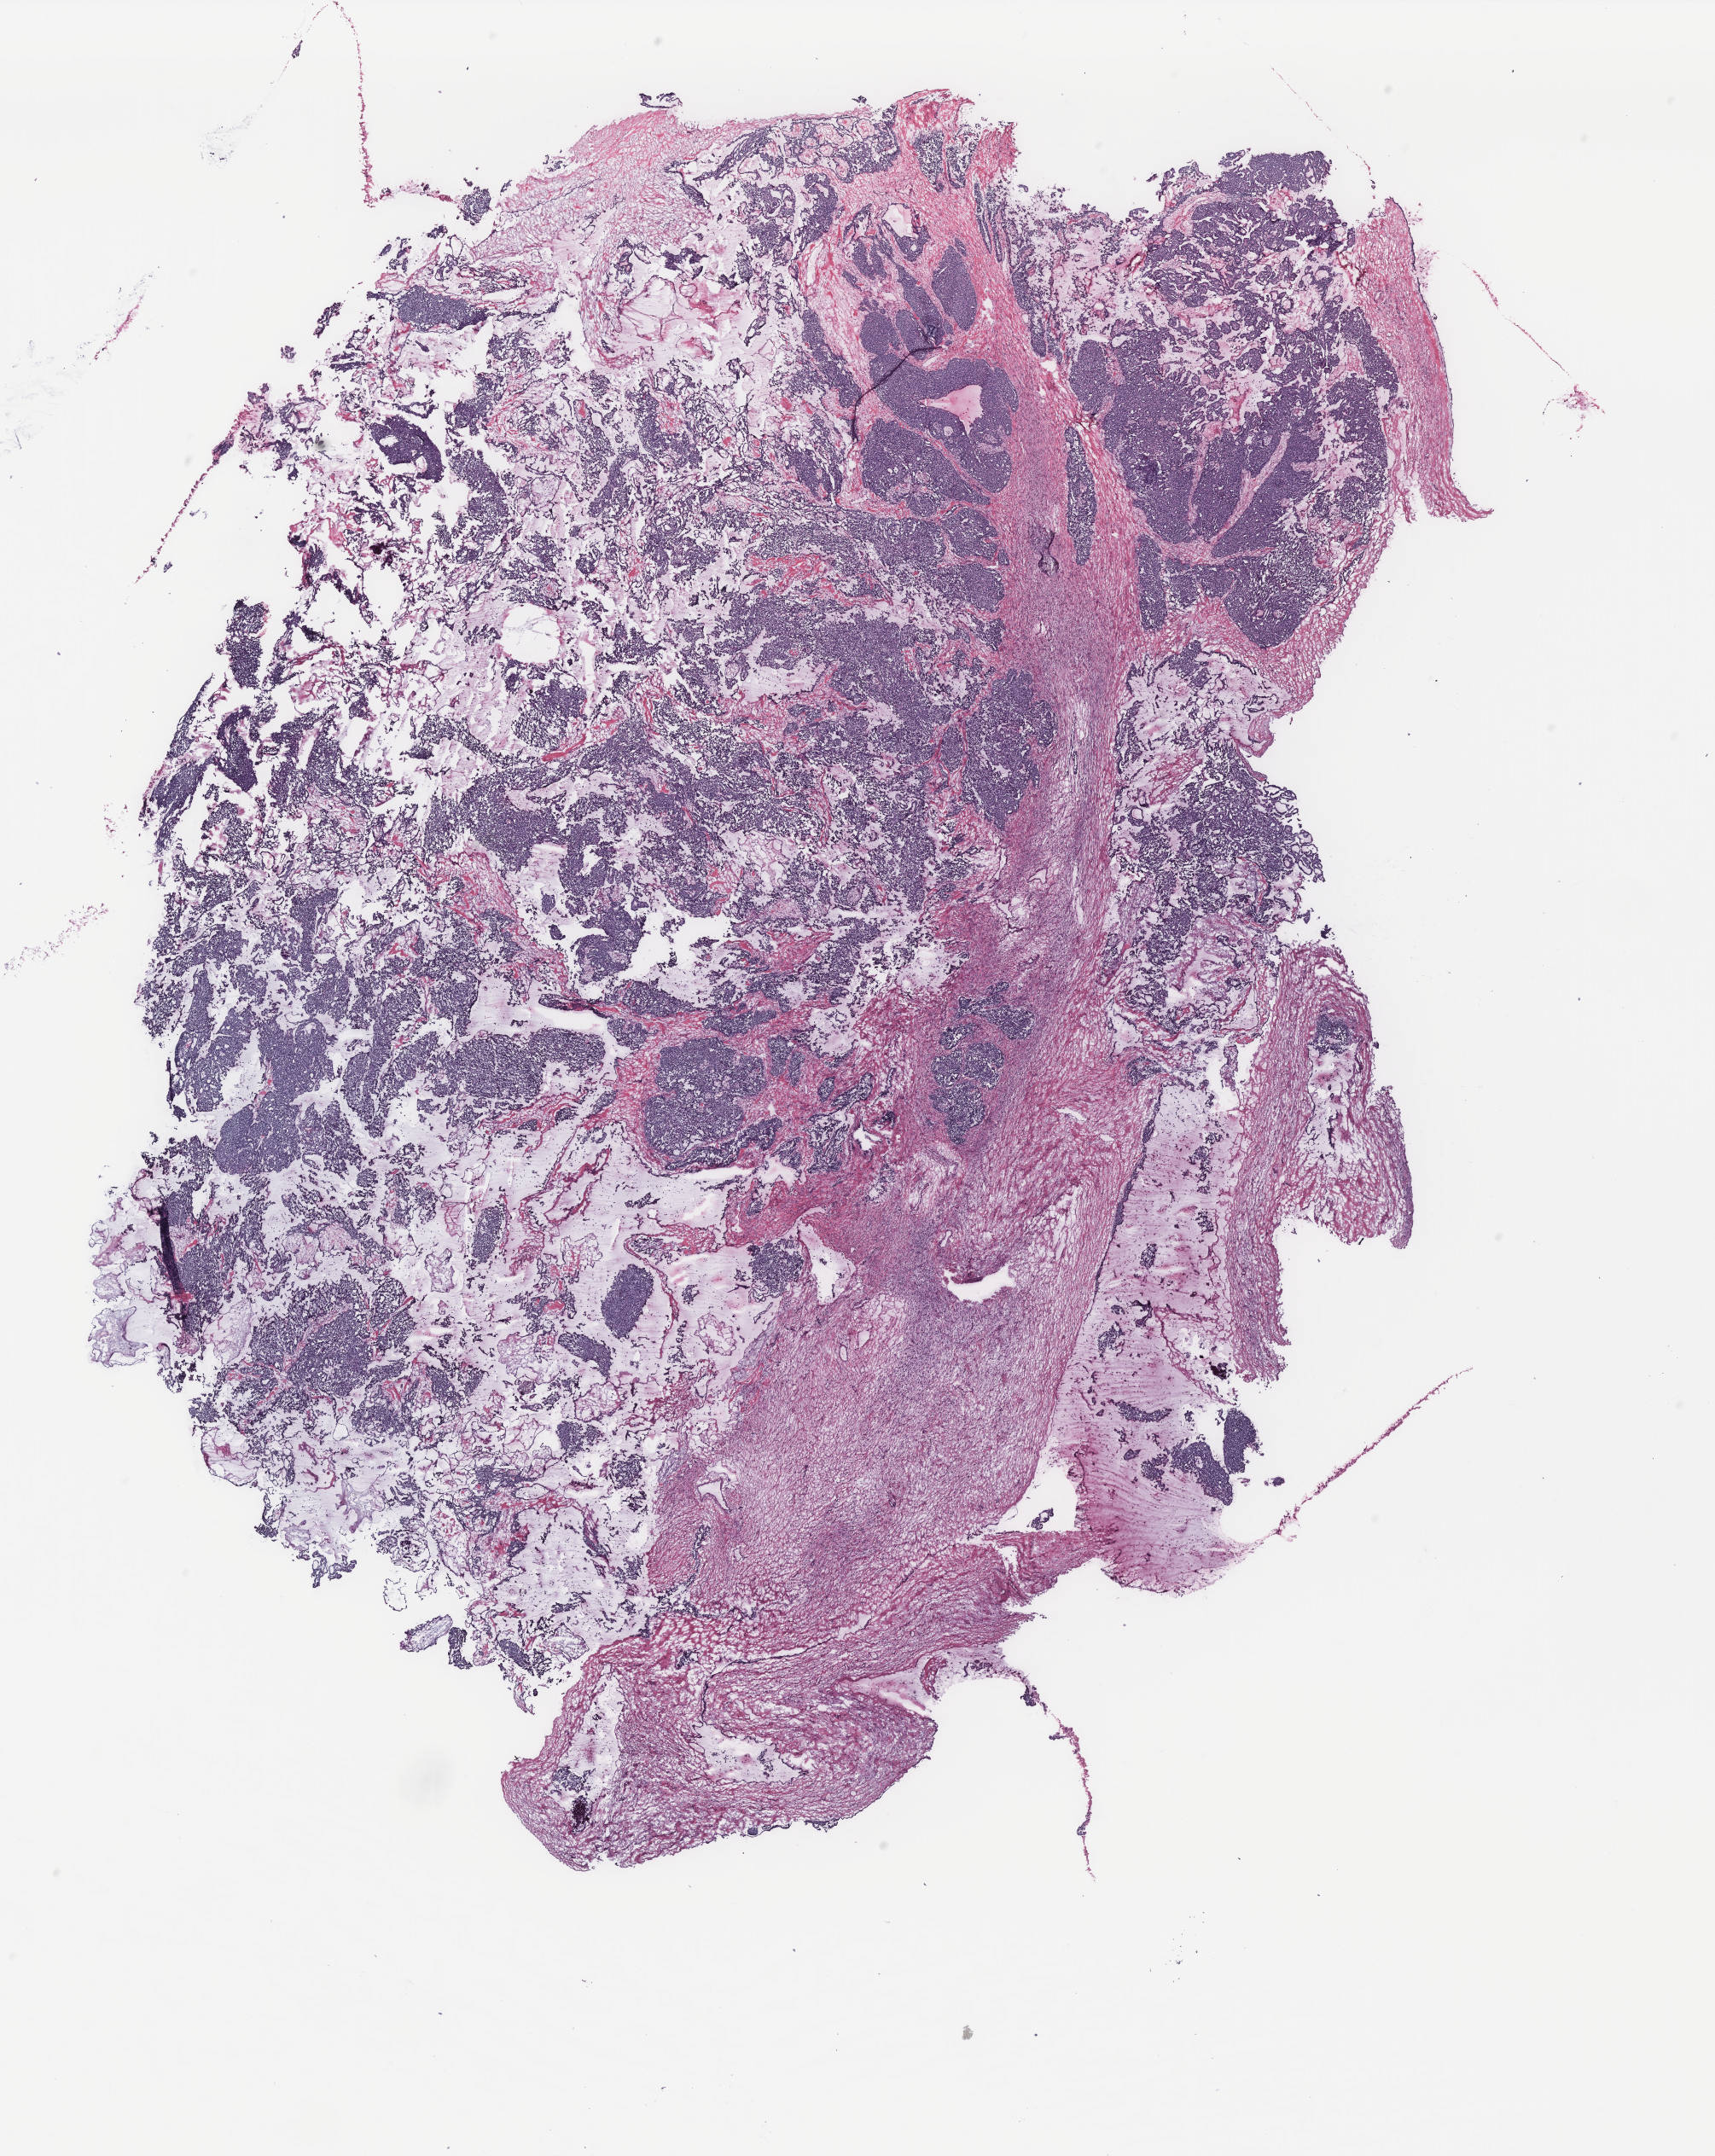
Whole-slide histology image, Hematoxylin and eosin (H&E) stained — low-resolution overview of the scanned area, about 16.1 x 20.2 mm, ovary, tissue type not recorded. Female patient.
Patient diagnosis: Serous adenocarcinoma, NOS.